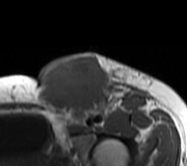
MRI of an extremity soft-tissue mass, one axial slice. Slice 41 of 62 in the series (ordered by position). MR volume resampled by the dataset authors to the PET/CT grid (not the native acquisition matrix). 187 × 166 image matrix, field of view 183 × 162 mm. Female patient. From the clinical record (not read from this slice): histological type: leiomyosarcoma; grade: high; site of the primary tumour: groin.
Annotated regions visible in this slice (expert contour drawn on MRI and transferred to this co-registered scan by the dataset authors):
- gross tumour volume including surrounding oedema: bounding box <36,53,149,127> (left, top, right, bottom; pixels)
- gross tumour volume (mass): <36,55,113,120>